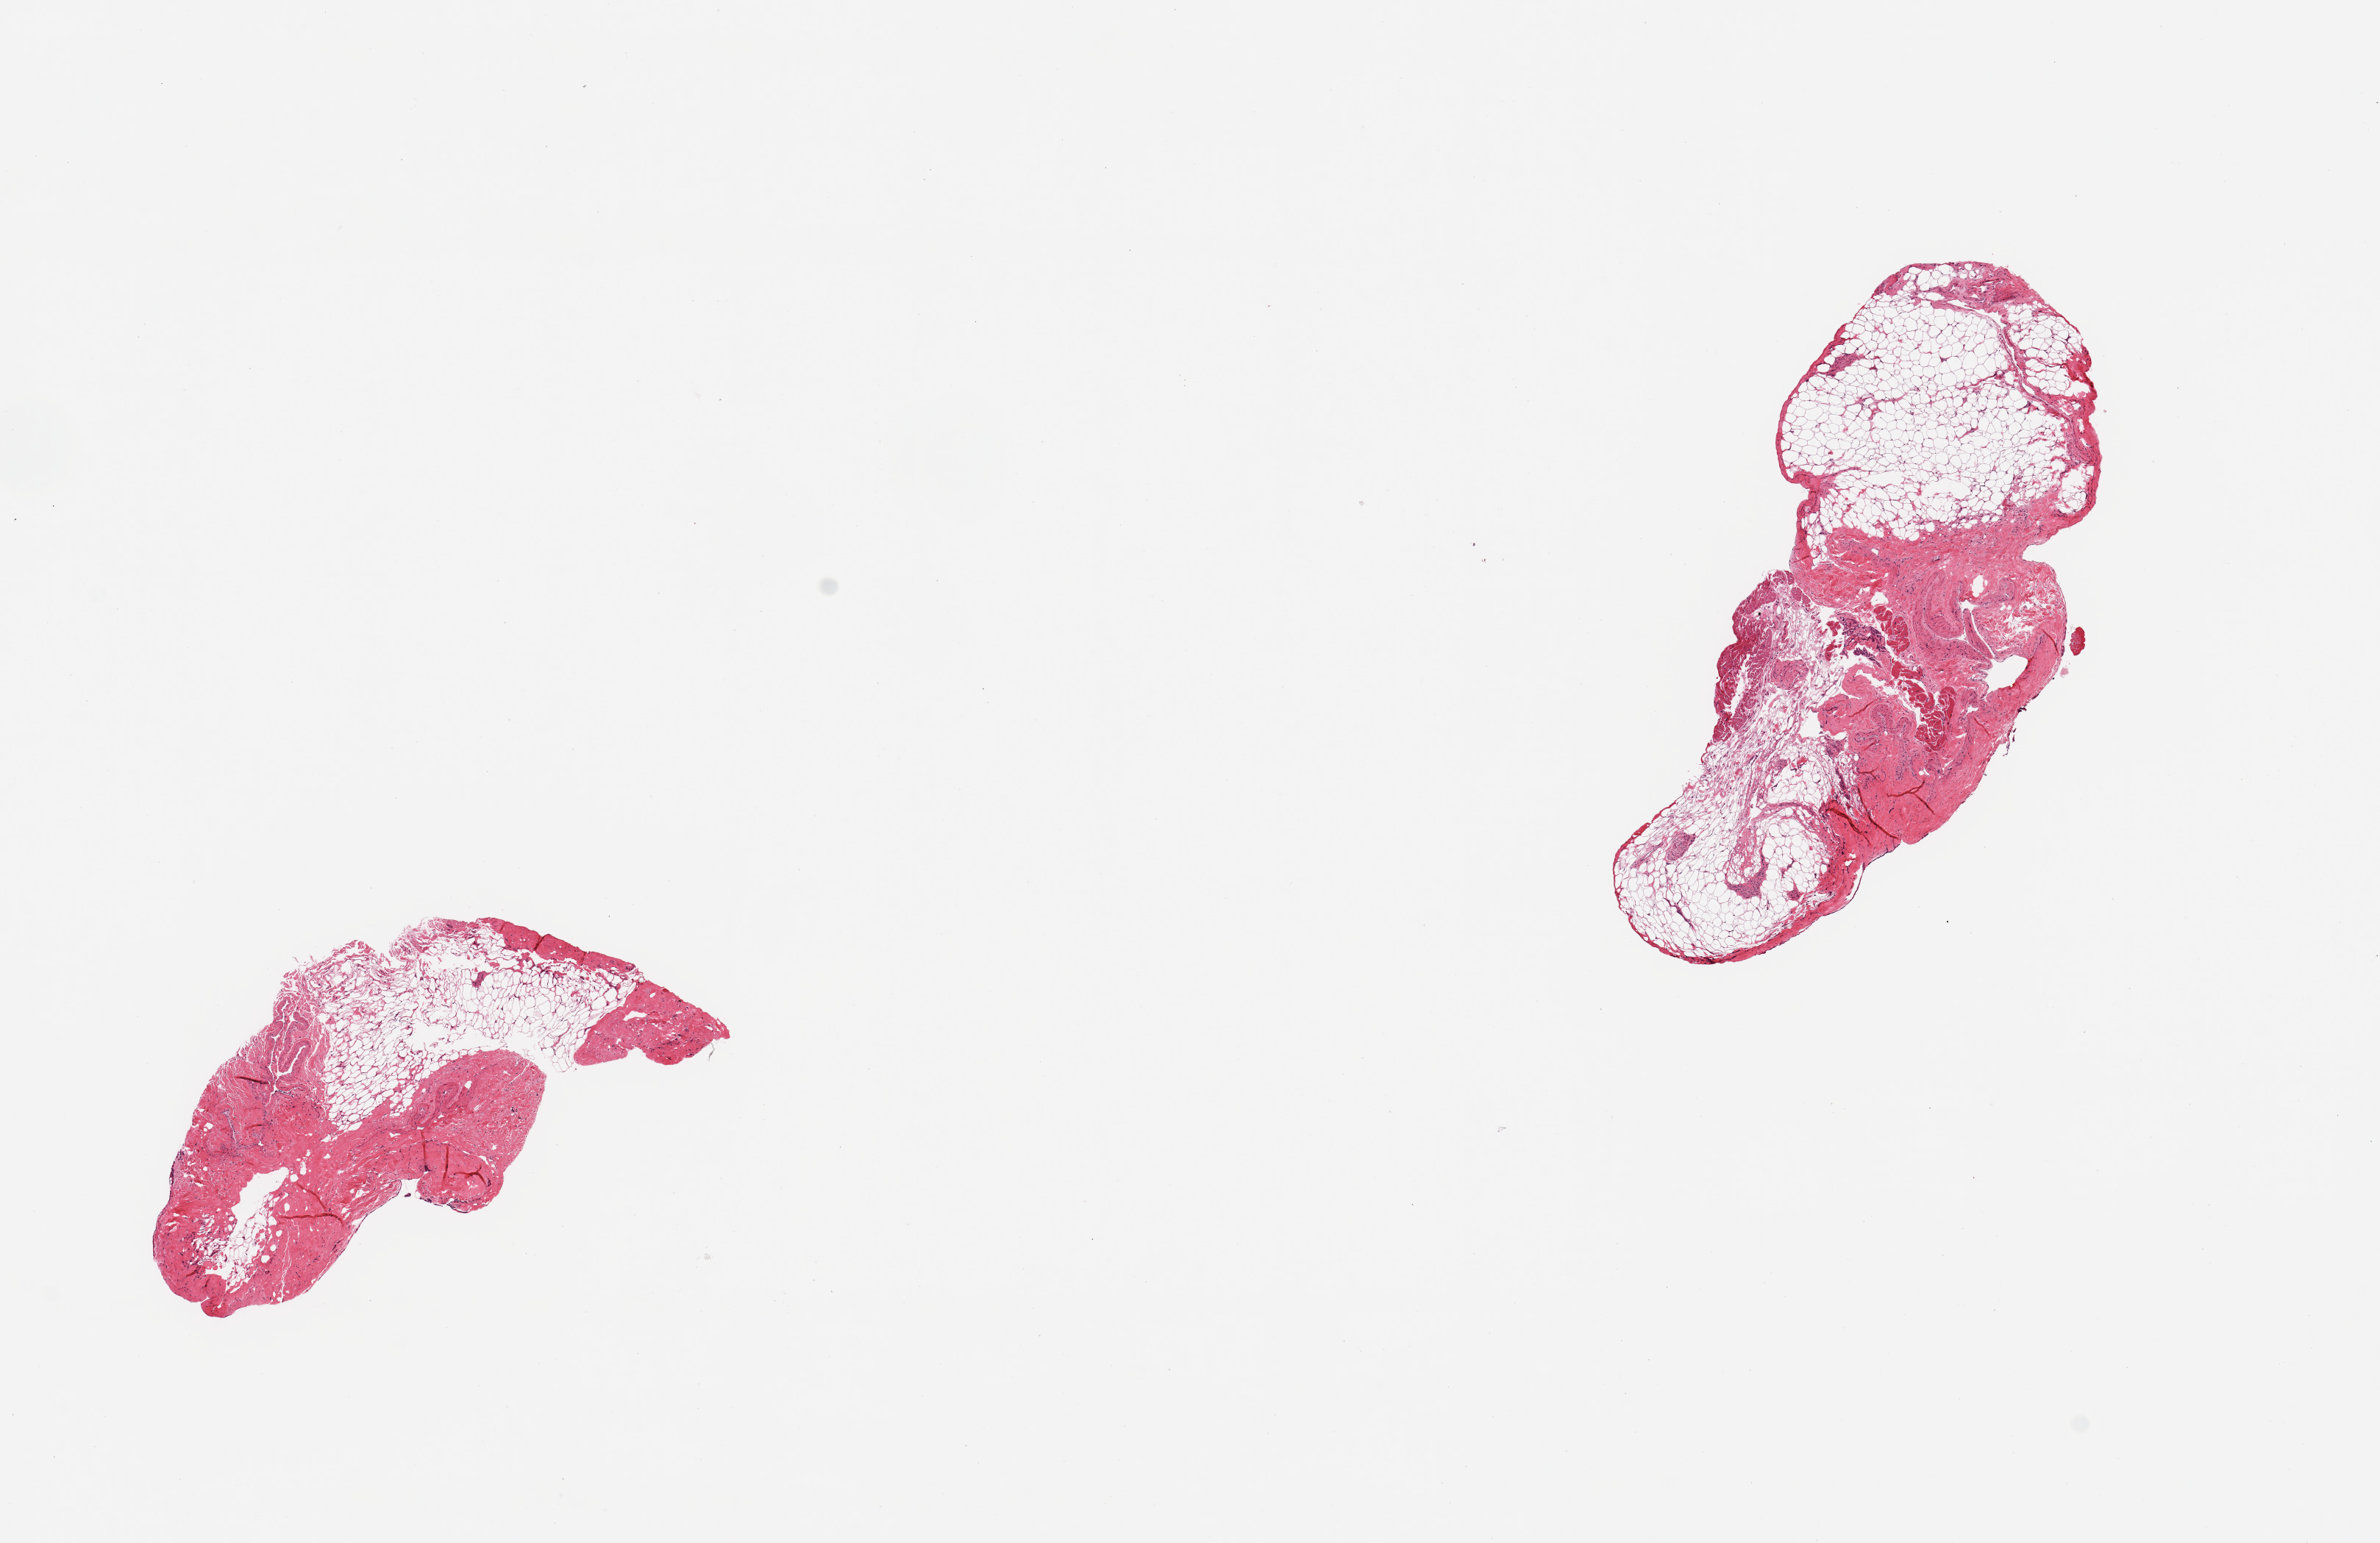
Digitized haematoxylin and eosin-stained section, low-resolution overview of the scanned area, about 12.8 x 8.3 mm. PAXgene-fixed paraffin-embedded (PFPE) section. Target tissue: coronary artery. Donor tissue sample.
Reviewer comment on this tissue sample: 2 pieces, fibroadipose connective tissues, no artery present.